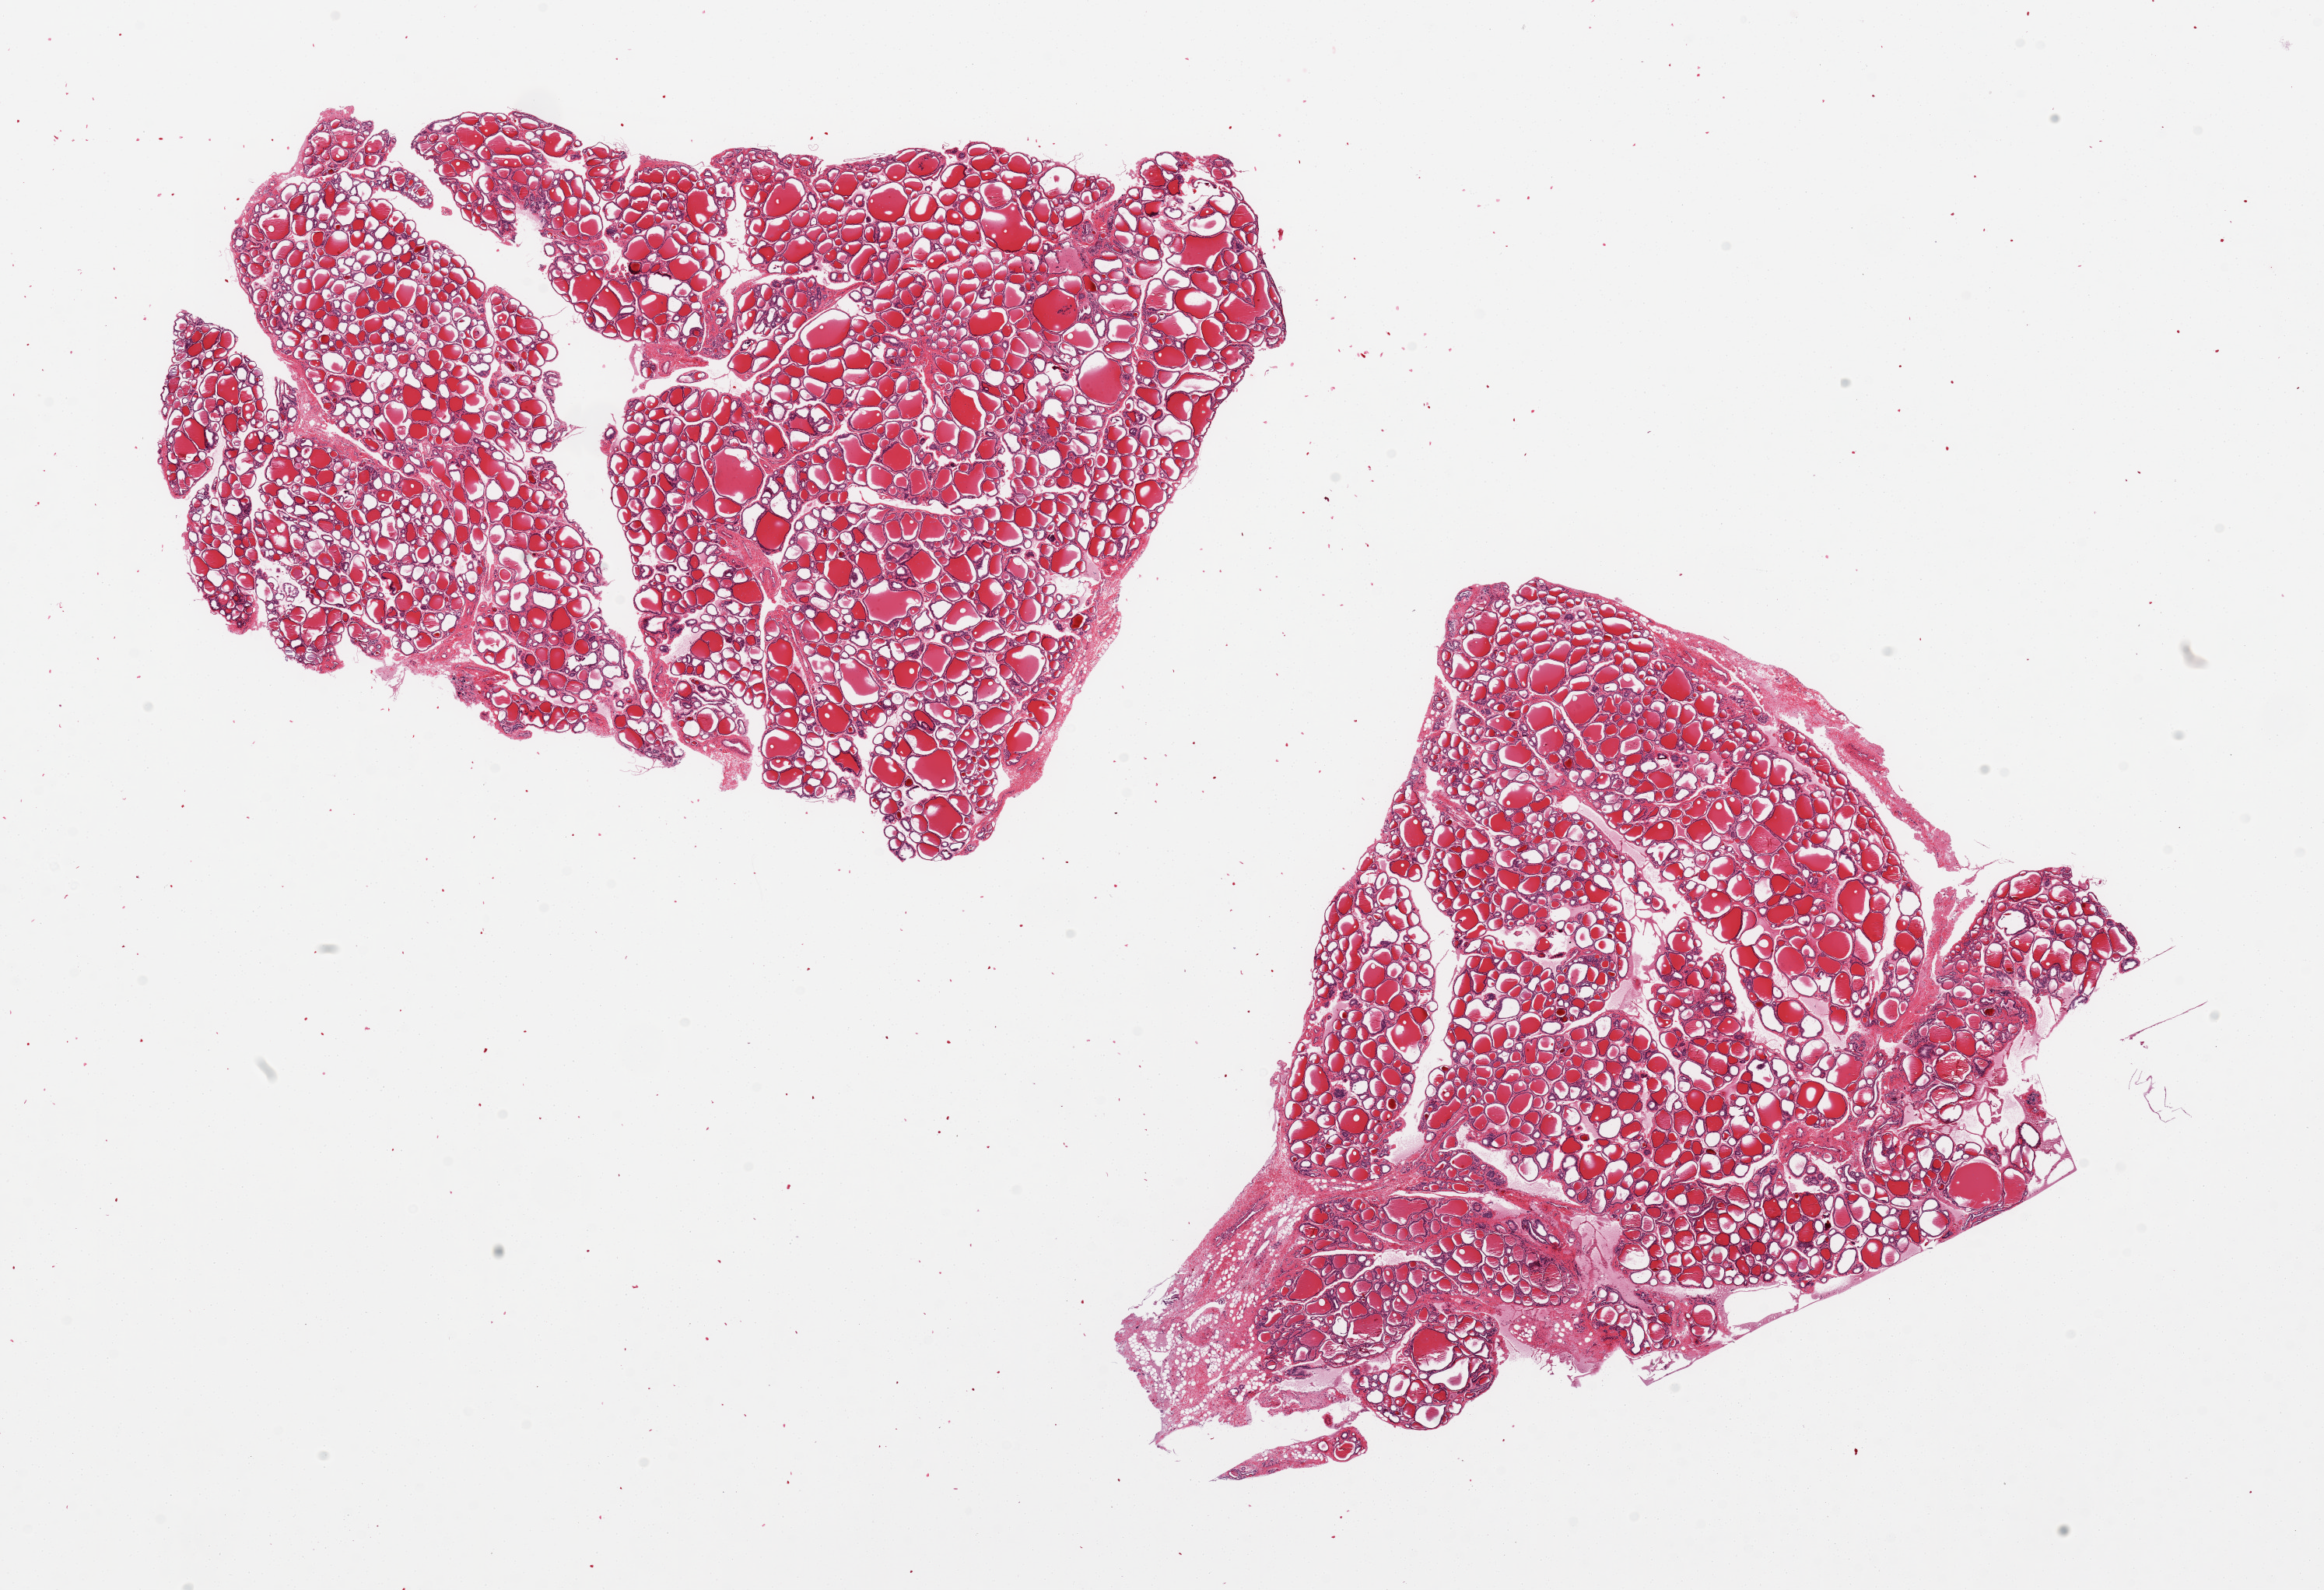
Whole-slide image, H&E stain, shown as a low-resolution overview of the whole scanned area (about 23.6 x 16.2 mm). PAXgene-fixed paraffin-embedded (PFPE) section. Section of thyroid (target tissue). Donor tissue sample. Donor sex: female.
- reviewer comment on this tissue sample: 2 pieces, small attachment of fibrofatty tissue